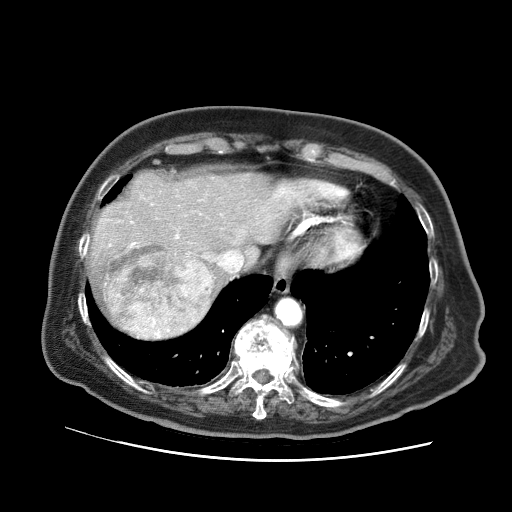
Contrast-enhanced abdominal CT (liver protocol), one axial slice; position 56 of 73 along the scan axis; soft-tissue window (W 400 / L 40 HU); 2.5 mm slice thickness; 512 × 512 image matrix, field of view 380 × 380 mm. Case-level facts recorded for this patient, not image findings: diagnosis: hepatocellular carcinoma (patient treated with transarterial chemoembolisation; whether this scan precedes or follows treatment is not stated here); TNM stage (as recorded): Stage-I; Child-Pugh class: A.
Structures marked on this image (semi-automatically segmented with operator editing):
- liver parenchyma outside the tumour (the mass and vessels are separate outlines, so this box may not span the whole liver): bounding box [x1, y1, x2, y2] px = [86, 172, 300, 339]
- mass: [104, 244, 215, 338]
- liver vessels: [130, 189, 287, 258]